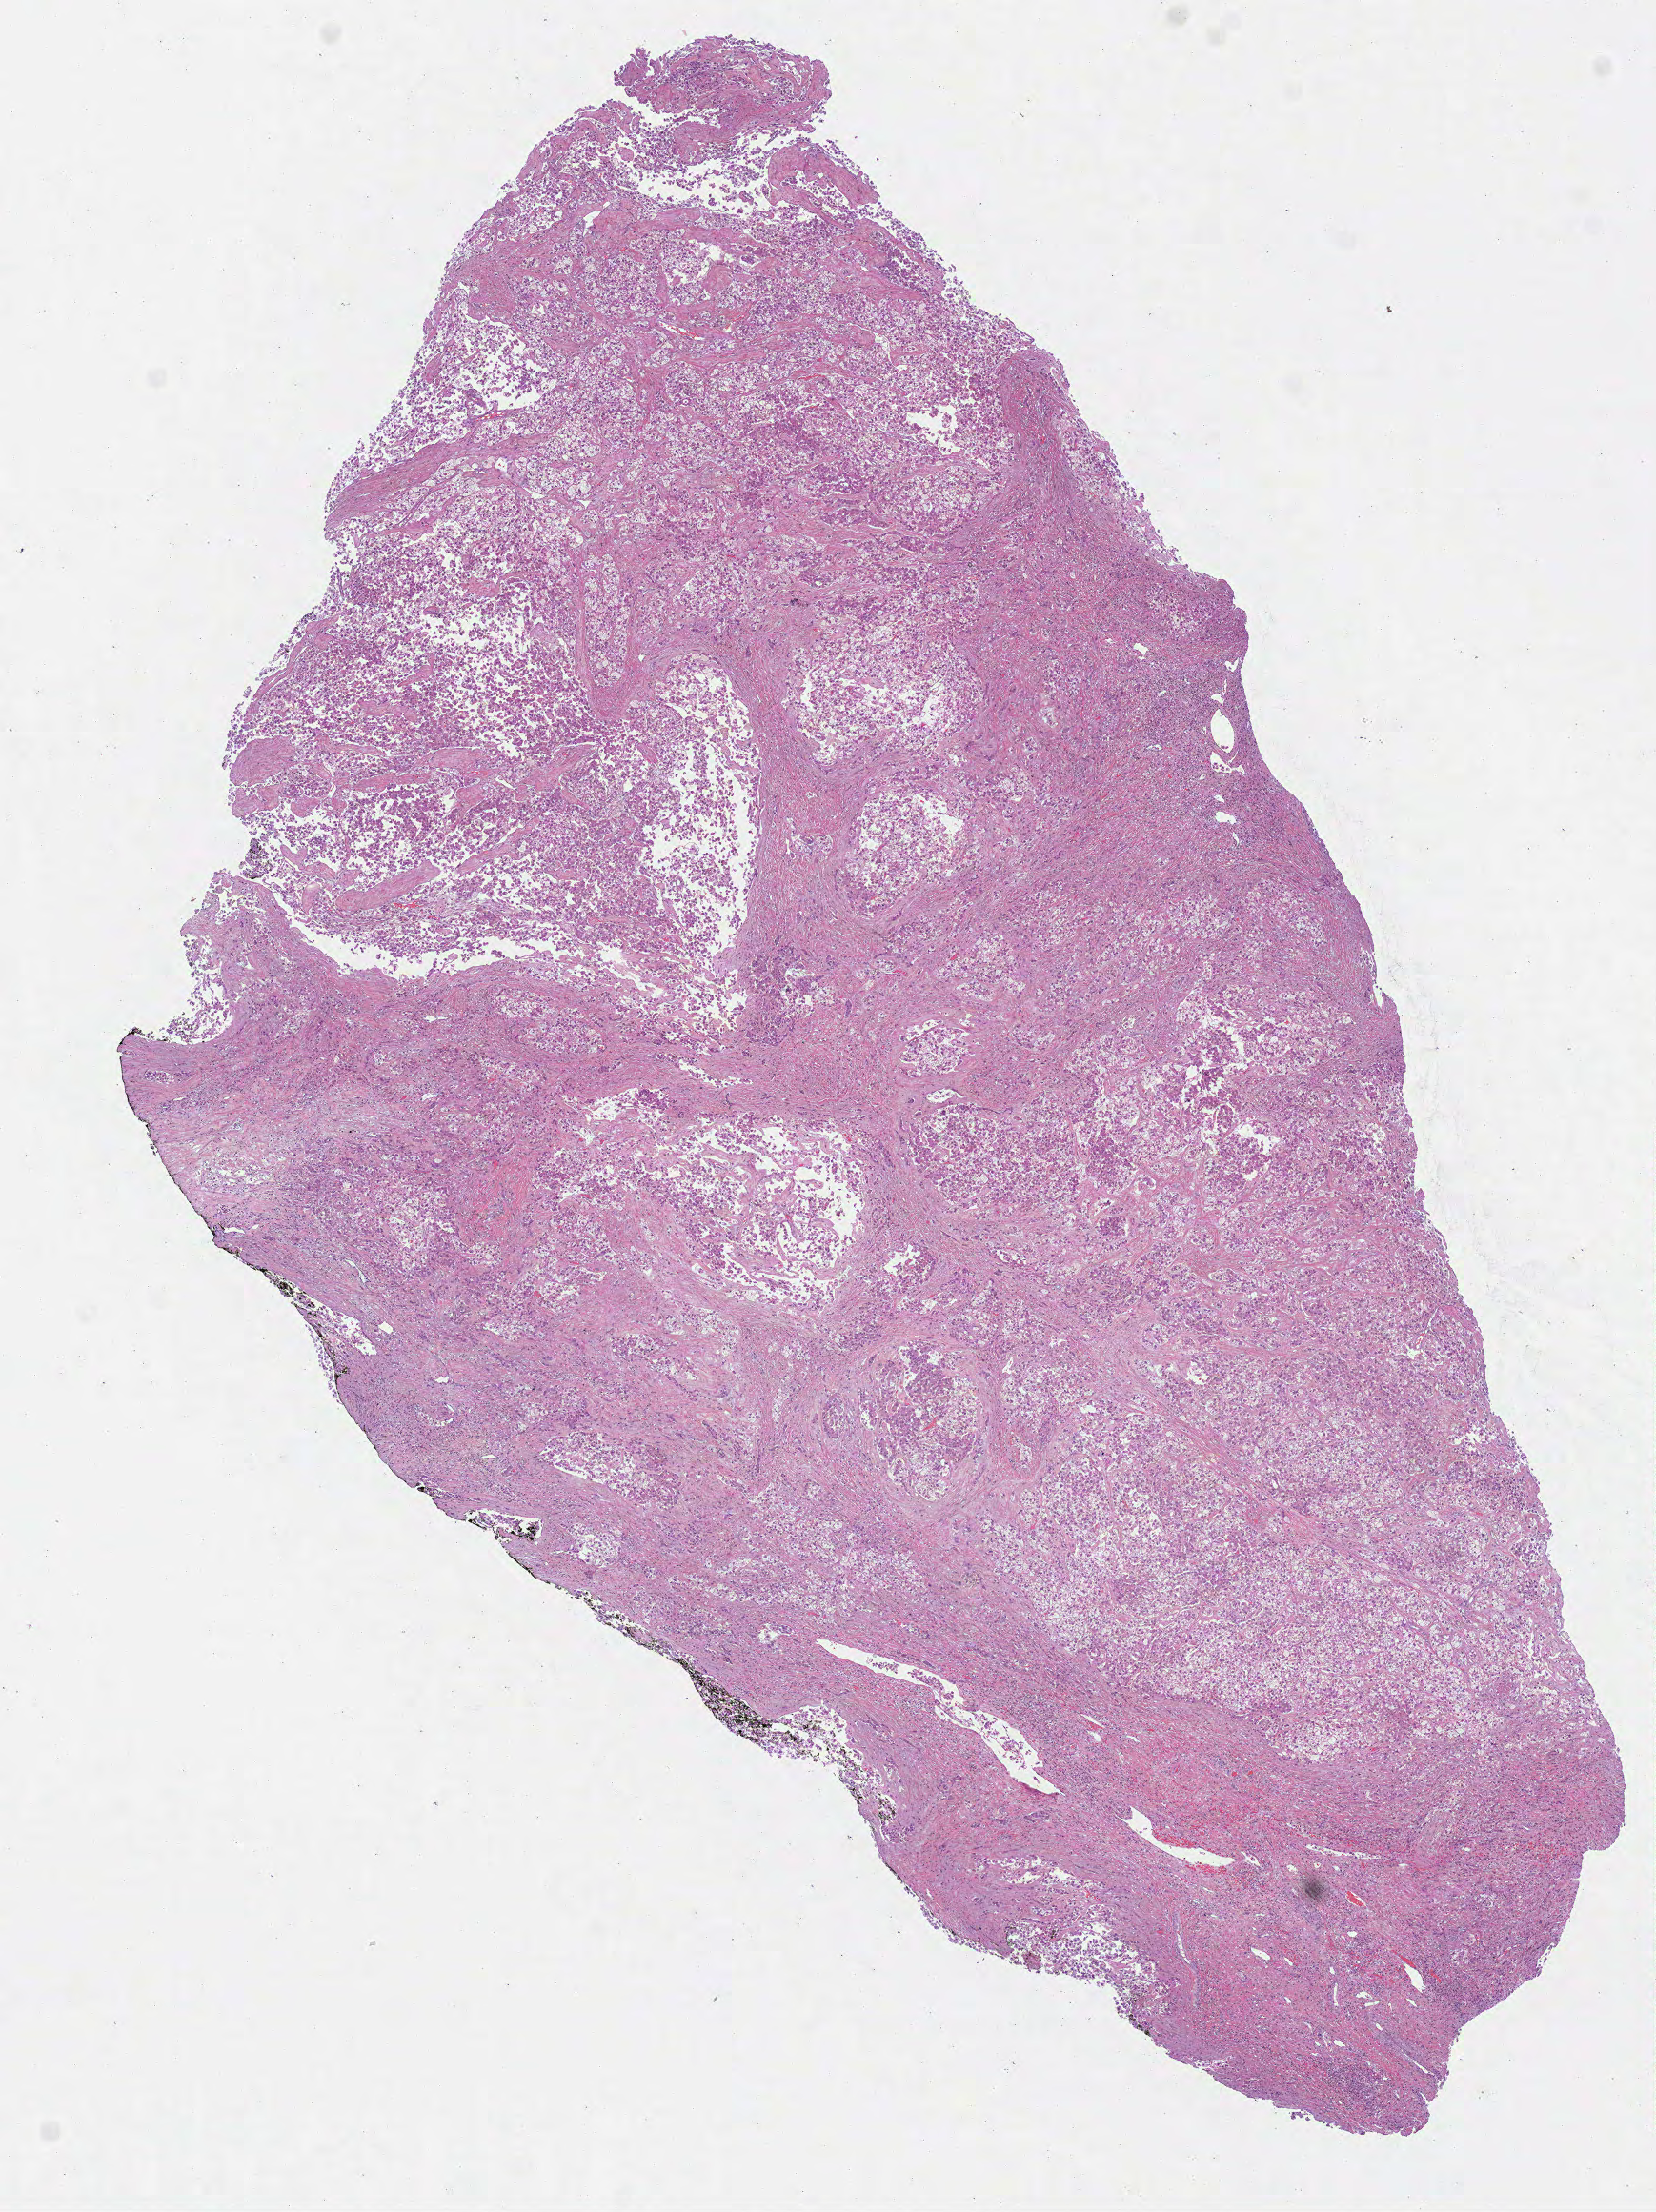
Whole-slide histology image, H&E — low-resolution overview of the scanned area, about 7.0 x 9.4 mm (from a 40x scan); formalin-fixed paraffin-embedded (FFPE) diagnostic section; sample: primary tumour, liver. Patient: male, age at initial diagnosis 75 years. Histologic grade: G1 (well differentiated).
• TNM: T1 N0 M0
• AJCC pathologic stage: I (6th edition)
• diagnosis: Hepatocellular carcinoma, NOS